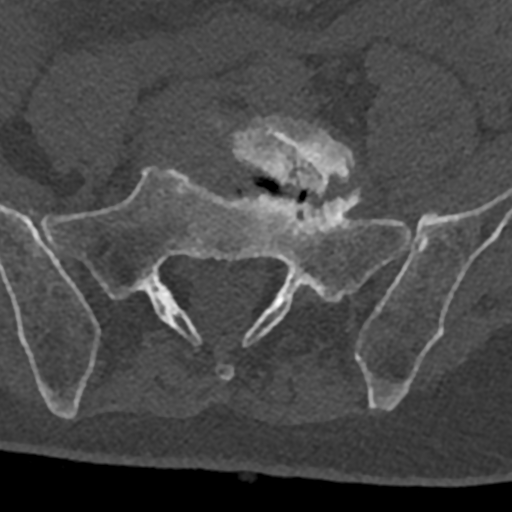
CT including the spine, one axial slice; position 157 of 797 along the scan axis; reconstruction kernel Br40s/3; 120 kVp; bone window (W 1800 / L 400 HU); 512 × 512 image matrix, field of view 160 × 160 mm. Patient: male, 74 years. Case-level facts recorded for this patient, not image findings: primary cancer: renal.
Annotated regions visible in this slice (semi-automatic segmentation, software-assisted and operator-edited):
- L5 vertebra: bounding box <218,115,355,197> (left, top, right, bottom; pixels)